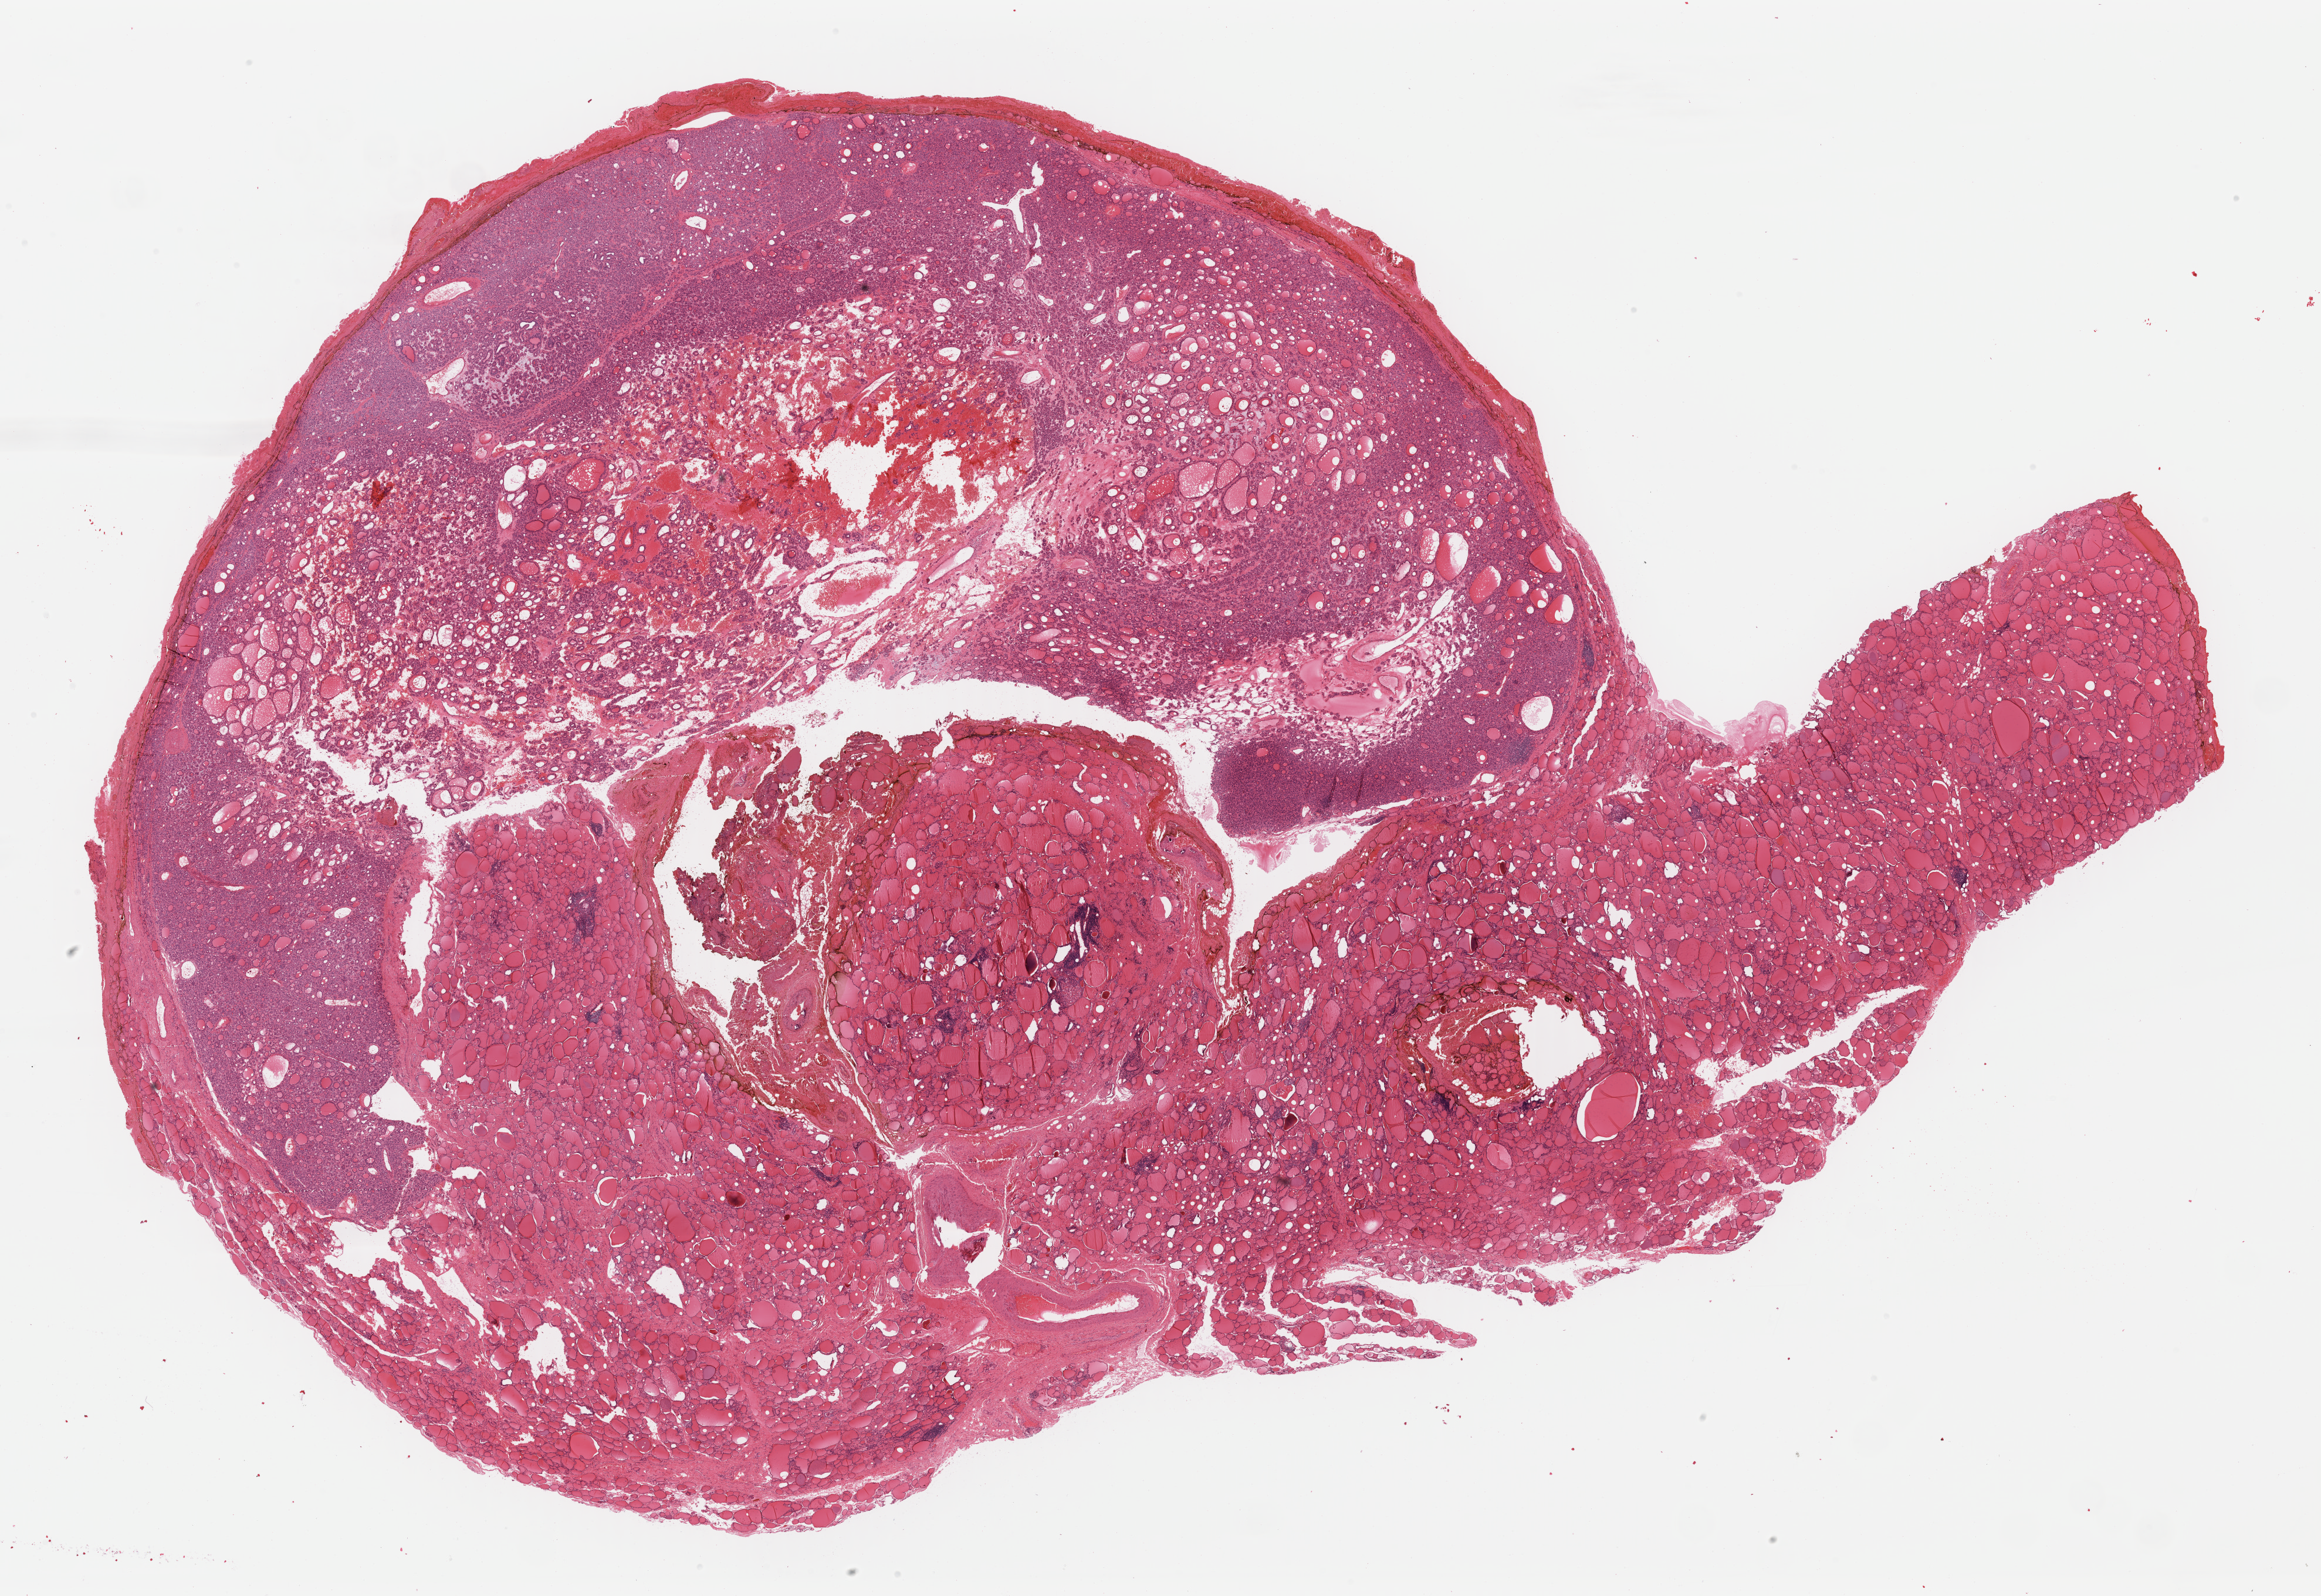
Digitized H&E tissue section (whole slide) — low-resolution overview of the scanned area, about 31.2 x 21.5 mm, FFPE section, primary tumour sample from the thyroid. Female patient; age at initial diagnosis 47 years.
- lymph nodes positive (case pathology): 0 of 3 examined
- AJCC pathologic stage: II
- histologic diagnosis: Papillary carcinoma, follicular variant (thyroid gland)